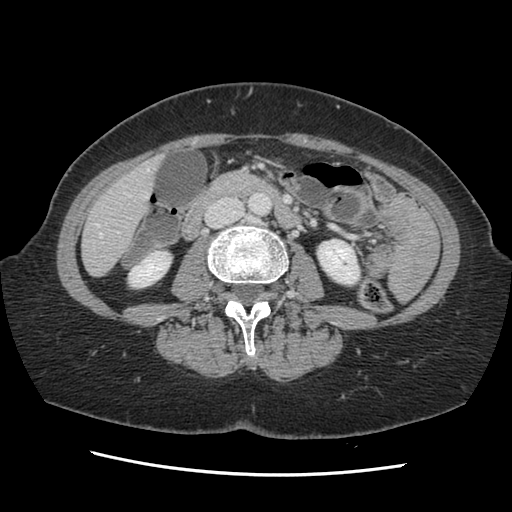
Contrast-enhanced abdominal CT, one axial slice. 120 kVp. Soft-tissue window (W 400 / L 40 HU). 2.5 mm slice thickness. 512 × 512 image matrix. Female patient, age 61 years. Case-level facts recorded for this patient, not image findings: diagnosis: colorectal cancer liver metastases, imaged before liver resection; multiple liver metastases: no; largest metastasis: 2.4 cm; disease in both lobes: no.
Outlined on this slice (expert manual segmentation):
- hepatic veins: box from (x=97, y=167) to (x=149, y=238) px
- liver: (x=83, y=159)–(x=160, y=276)
- planned liver remnant (the part of the liver to remain after resection): (x=83, y=165)–(x=157, y=276)